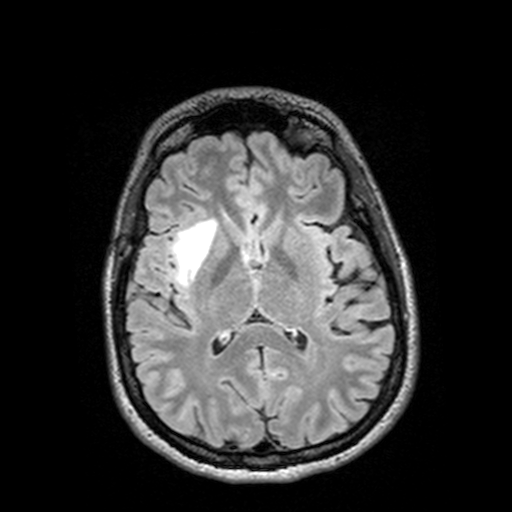
Brain MRI from a brain-tumour surgery series, one axial slice. Position 66 of 144 along the scan axis. T2 FLAIR. 512 × 512 image matrix, field of view 250 × 250 mm. Case-level facts recorded for this patient, not image findings: histopathology: Astrocytoma; WHO grade: 3; IDH mutation: yes; tumour location: Right Insular Temporal.
Annotated regions visible in this slice (expert manual segmentation):
- tumour: bounding box <126,222,232,286> (left, top, right, bottom; pixels)